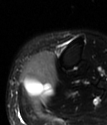
MRI of an extremity soft-tissue mass, one axial slice; position 23 of 78 along the scan axis; T2-weighted fat-saturated; MR volume resampled by the dataset authors to the PET/CT grid (not the native acquisition matrix); 3.27 mm slice thickness; 107 × 125 image matrix. Female patient. From the clinical record (not read from this slice): histological type: extraskeletal high grade osteogenic sarcoma; grade: high; site of the primary tumour: left calf.
Annotated regions visible in this slice (expert contour drawn on MRI and transferred to this co-registered scan by the dataset authors):
- gross tumour volume (mass): bounding box <21,52,56,99> (left, top, right, bottom; pixels)